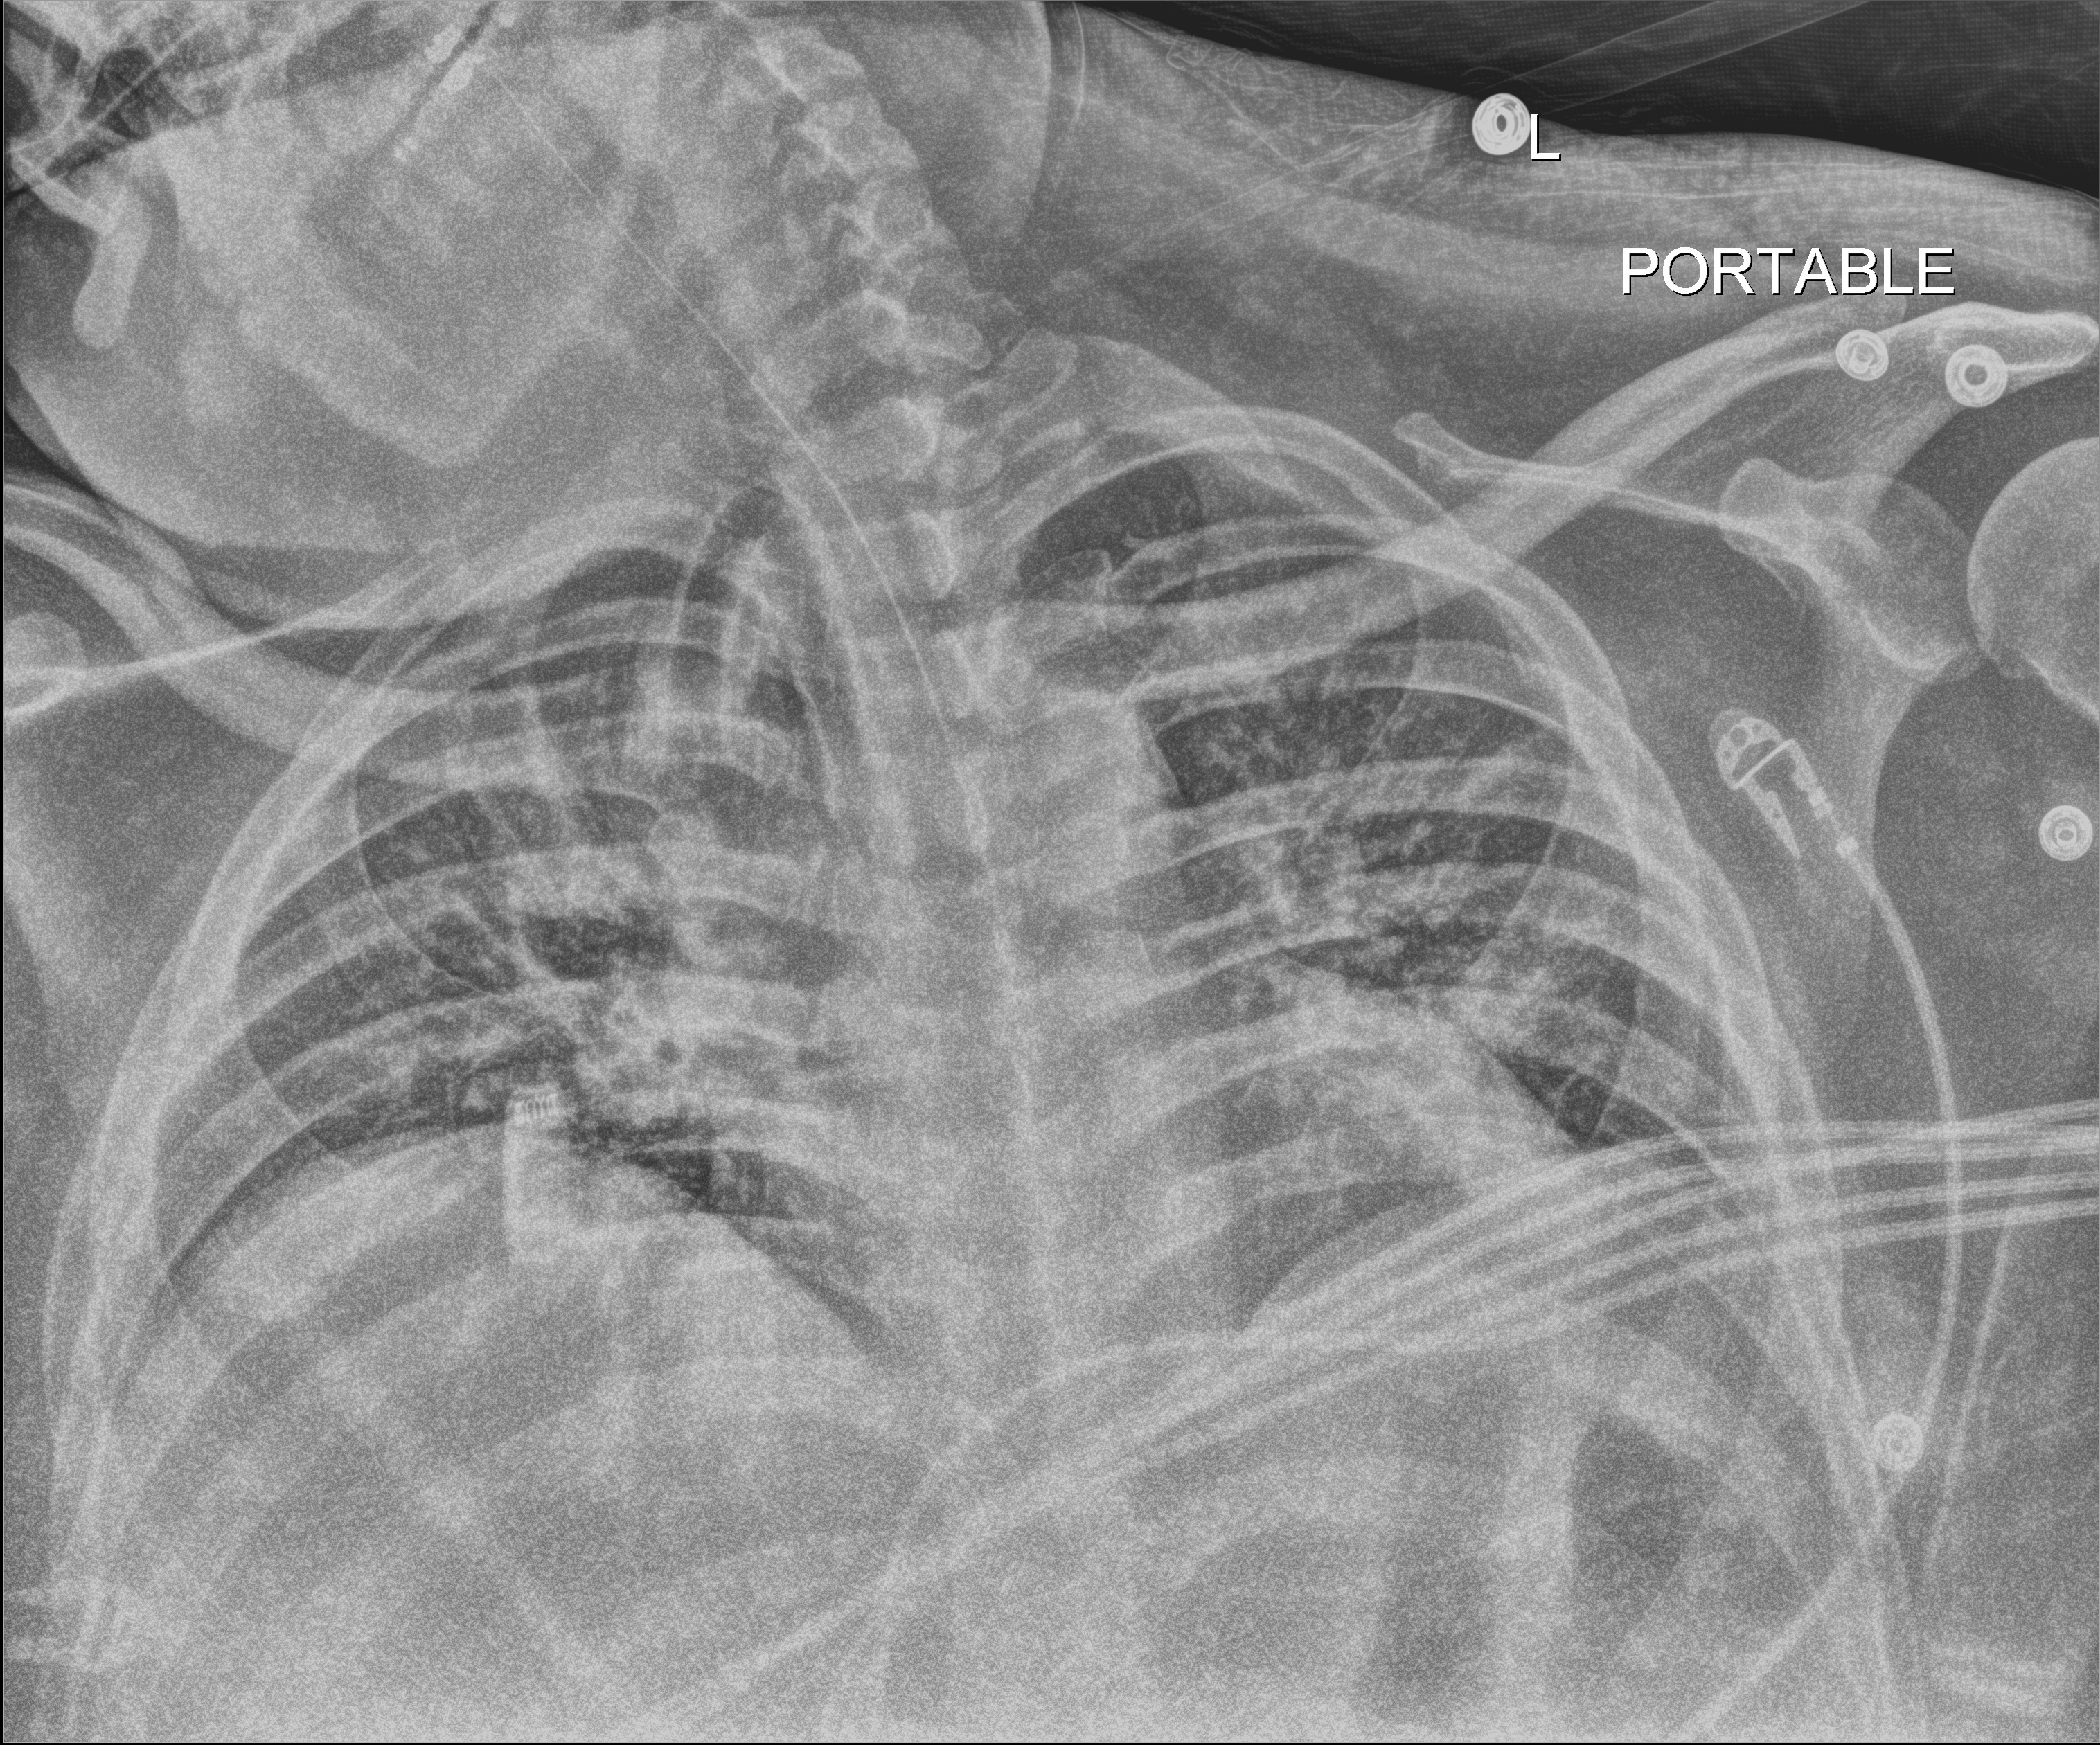
Chest X-ray (portable); anteroposterior (AP) projection. Male patient hospitalised with COVID-19, age 18–59 years.
Hospital-stay facts (about this admission, not read from this image; timing relative to this image not recorded):
- admitted to intensive care during this hospital stay: yes
- chronic kidney disease (admission record): no